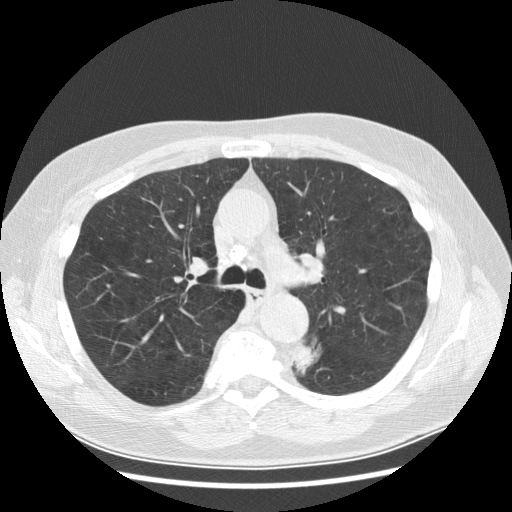
Low-dose screening chest CT, one axial slice; position 189 of 282 along the scan axis; reconstruction kernel STANDARD; lung window (W 1500 / L -600 HU); 512 × 512 image matrix.
Annotated regions visible in this slice (manually delineated by an expert):
- lesion 1 (tumor, lower lobe of left lung): box from (x=293, y=339) to (x=321, y=375) px